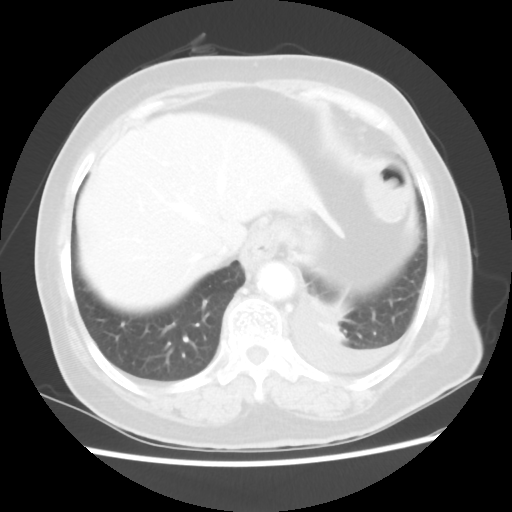
Chest CT, one axial slice; slice 8 of 80 in the series (ordered by position); lung window (W 1500 / L -600 HU); 5 mm slice thickness; 512 × 512 image matrix, field of view 343 × 343 mm. Patient: female, 68 years. From the clinical record (not read from this slice): clinical TNM (as recorded): T1c N0 M1.
Annotated regions visible in this slice (bounding box drawn by a radiologist):
- lung tumour (recorded histology: adenocarcinoma): bounding box <312,296,359,344> (left, top, right, bottom; pixels)